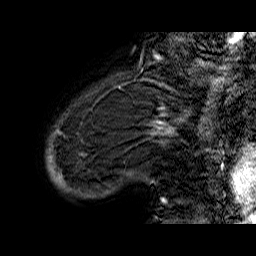
Breast MRI (dynamic contrast-enhanced), one sagittal slice; position 6 of 60 along the scan axis; dynamic contrast-enhanced series, time point 2 of 6 at this slice position (early post-contrast); 1.5 T; TE 6.5 ms, TR 32.9 ms; 4 mm slice thickness; 256 × 256 image matrix, field of view 200 × 200 mm. Female patient. From the clinical record (not read from this slice): setting: breast cancer imaged before/during neoadjuvant chemotherapy; receptor status: HR-positive, HER2-negative.
Annotated regions visible in this slice (semi-automatically segmented with operator editing):
- analysis volume of interest (the breast-tissue region the enhancement analysis was run in; not a lesion): box from (x=45, y=74) to (x=176, y=208) px
- tumour enhancement mask (voxels above the 100 % enhancement threshold inside the analysis volume of interest): (x=162, y=122)–(x=167, y=205)